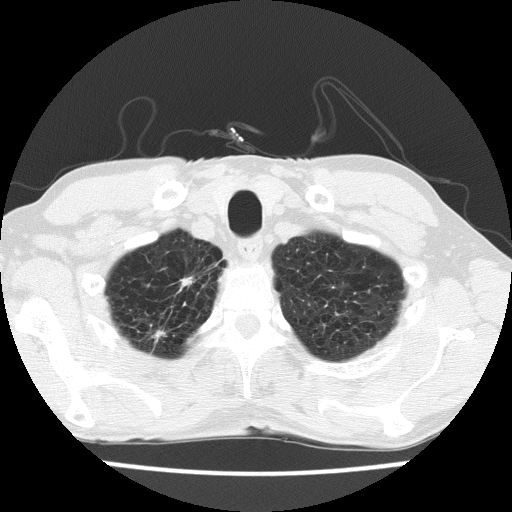
Chest CT (low-dose screening protocol), one axial image, second screening round (one year after baseline), lung window (W 1500 / L -600 HU), 2 mm slice thickness, lung (sharp) reconstruction kernel (FC51), slice 19 of 175 in the series, 512 × 512 image matrix, field of view 326 × 326 mm. Male, age 63 years at enrolment. Current smoker at enrolment.
• Expert-annotated lung lesion, bounding box <137,262,205,332> (left, top, right, bottom; pixels).
• Screening reader's record for this exam: no non-calcified nodule ≥4 mm recorded.
• Participant outcome: lung cancer diagnosed 390 days after this screen (after the third annual screen) — adenocarcinoma, NOS, right upper lobe, moderately differentiated (G2), stage IIIB (AJCC 6th edition), 17 mm at pathology.